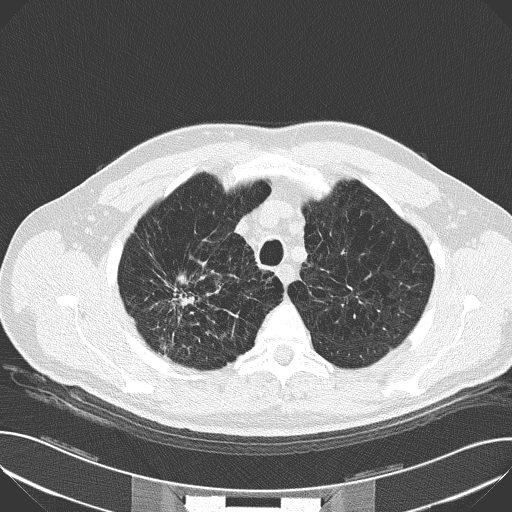
Axial slice from a low-dose chest CT screening exam. Baseline annual screen. Lung window (W 1500 / L -600 HU). Slice 28 of 159 in the series. Male participant, aged 59 years at enrolment. Current smoker at enrolment.
- Lesion marked by an expert reader, bounding box (x1, y1, x2, y2) in pixels: (153, 259, 215, 326).
- The screening reader recorded 4 non-calcified nodules or masses ≥4 mm on this exam (right upper lobe, left upper lobe, right upper lobe, left upper lobe); which of them this box marks is not recorded.
- Official screen result: positive, change unspecified: nodule(s) >= 4 mm or enlarging nodule(s), mass(es), or other non-specific abnormalities suspicious for lung cancer.